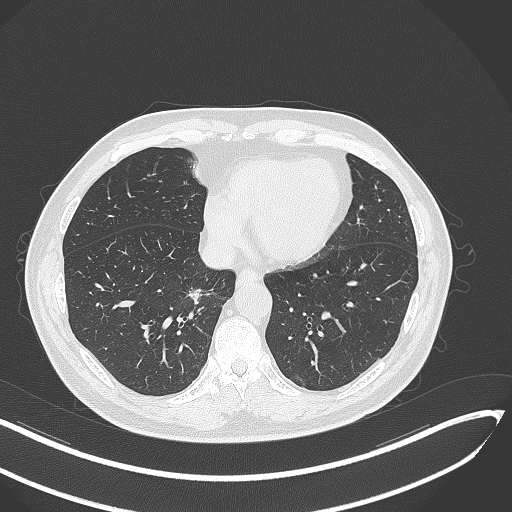
Chest CT, one axial slice; slice 121 of 429 in the series (ordered by position); 120 kVp; lung window (W 1500 / L -600 HU); 512 × 512 image matrix. Male patient, age 62 years. From the clinical record (not read from this slice): clinical TNM (as recorded): T1b N0 M0; histopathological grade: G2.
Annotated regions visible in this slice (bounding box drawn by a radiologist):
- lung tumour (recorded histology: adenocarcinoma): bounding box <183,286,211,313> (left, top, right, bottom; pixels)